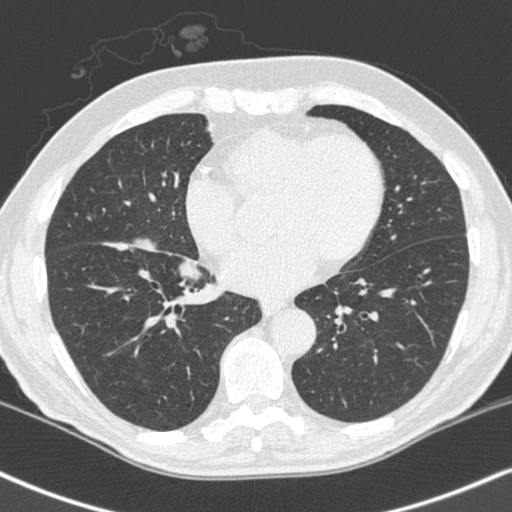
Low-dose screening chest CT, axial slice; baseline annual screen; lung window (W 1500 / L -600 HU); 1.3 mm slice thickness; 512 × 512 image matrix, field of view 323 × 323 mm. Male participant, aged 68 years at enrolment. Current smoker at enrolment.
Expert reader's lesion annotation, bounding box <90,230,166,302> (left, top, right, bottom; pixels). The exam's reader record, not a measurement of the box and not confirmed to be the same lesion: non-calcified nodule or mass ≥4 mm, right lower lobe, 34 × 17 mm, smooth margins, soft tissue attenuation.